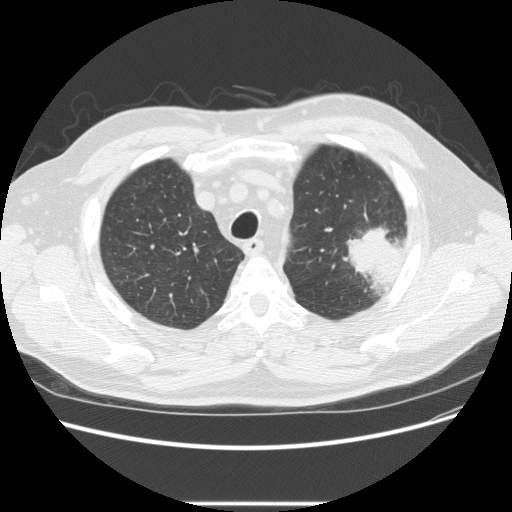
Chest CT (low-dose screening protocol), one axial image; baseline annual screen; lung window (W 1500 / L -600 HU); 2.5 mm slice thickness; slice 51 of 233 in the series; 512 × 512 image matrix. Male participant, aged 73 years at enrolment.
• Expert-annotated lung lesion, bounding box <332,216,411,285> (left, top, right, bottom; pixels).
• The screening reader recorded 2 non-calcified nodules or masses ≥4 mm on this exam (left upper lobe, right upper lobe); which of them this box marks is not recorded.
• Later outcome: lung cancer diagnosed 11 days after this screen — bronchiolo-alveolar adenocarcinoma, NOS, other location, well differentiated (G1), stage IV (AJCC 6th edition).